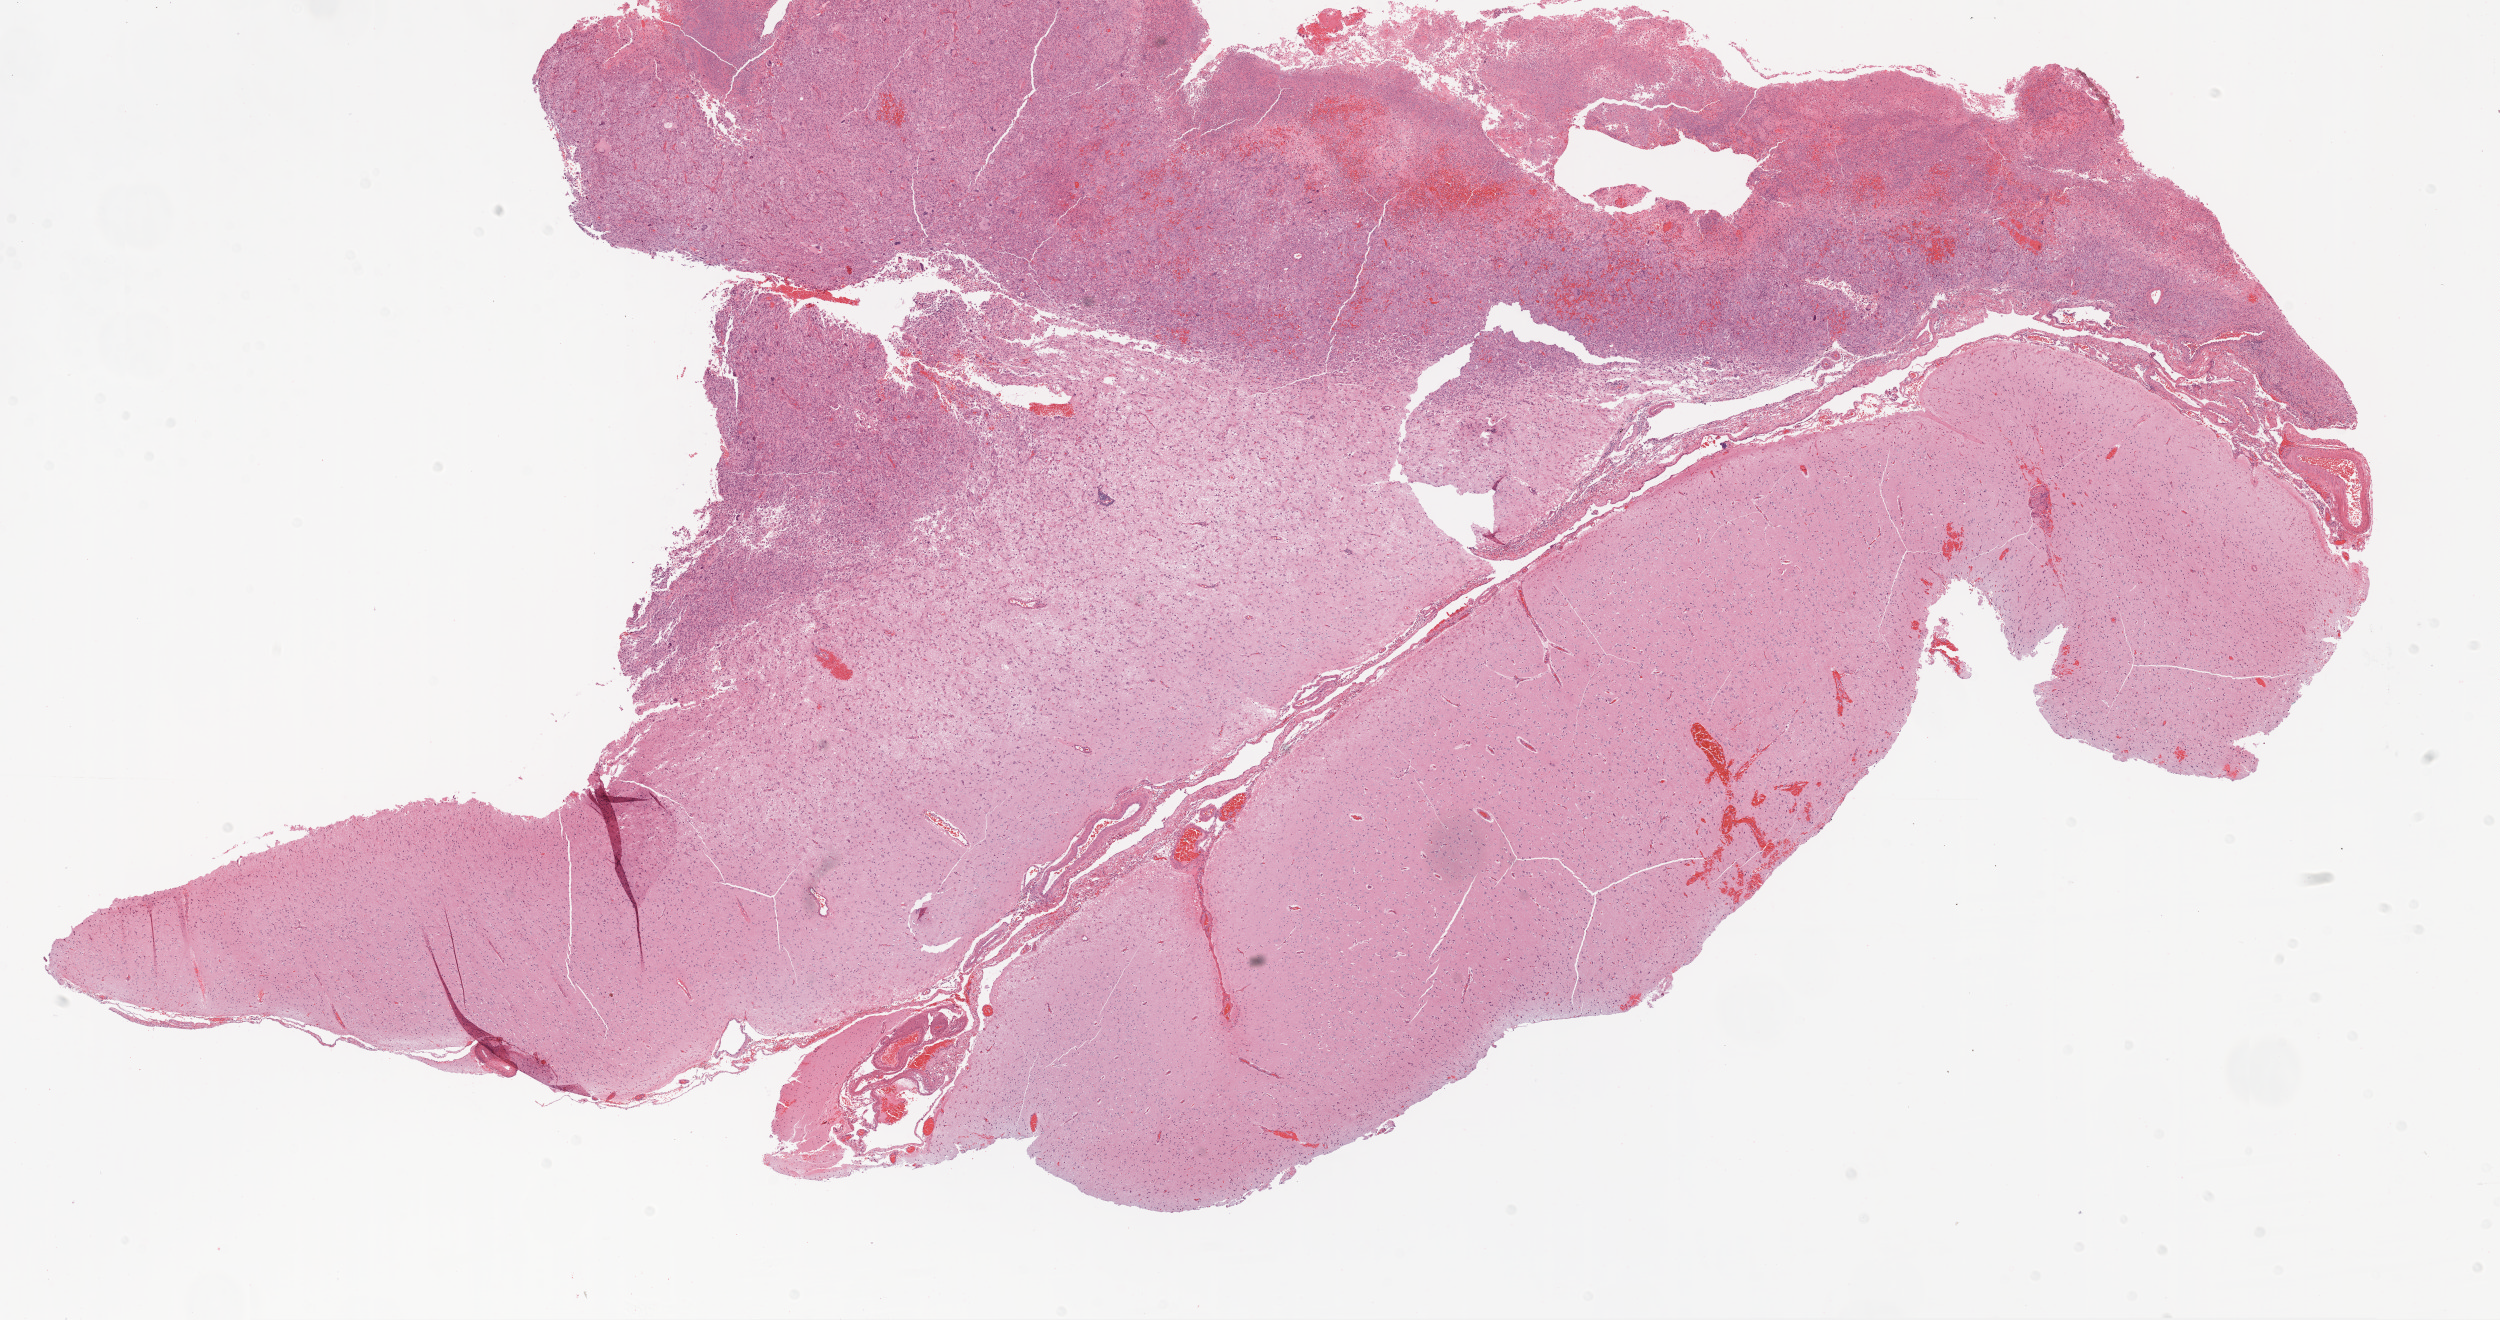
Whole-slide histology image, H&E, whole scanned area (about 20.1 x 10.6 mm, acquisition: 20x scan) shown as a low-resolution overview; FFPE section; brain, primary tumour sample. Patient: male, age at initial diagnosis 34 years.
Pathologic diagnosis: Glioblastoma.